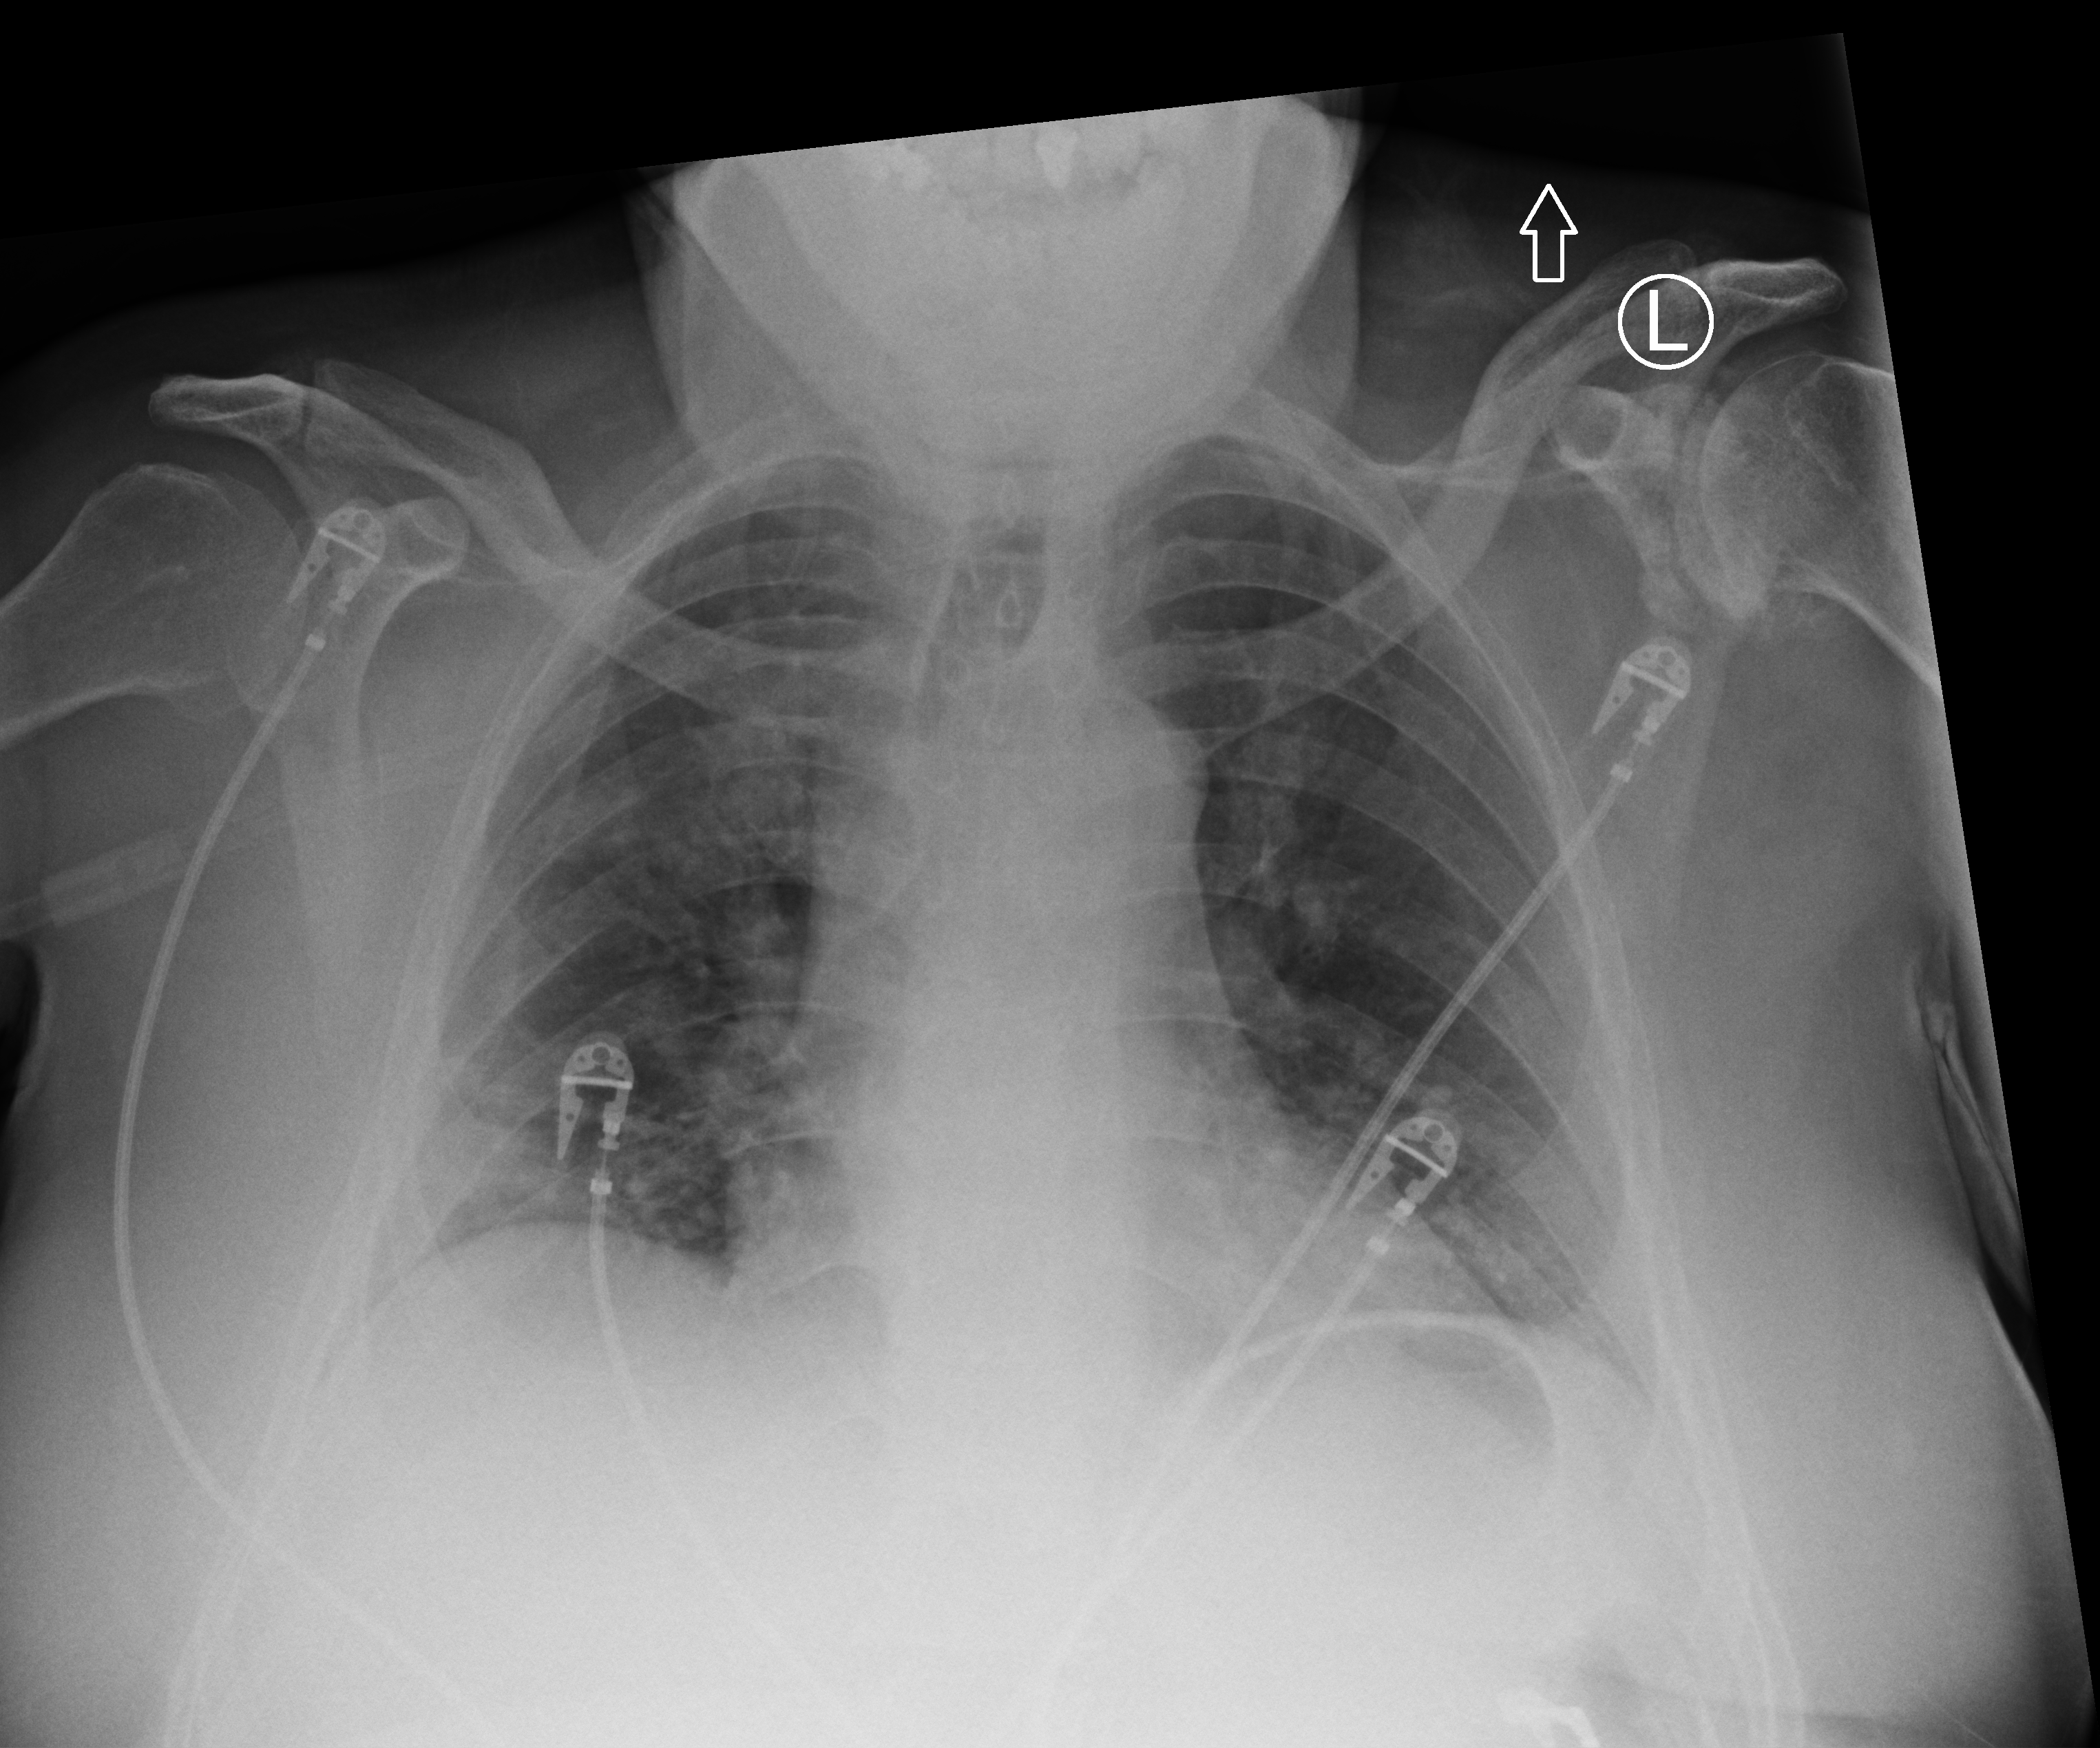
Chest X-ray (portable), anteroposterior (AP) projection. Male patient hospitalised with COVID-19, age 60–74 years.
Admission-level facts for this patient (not findings on this image; timing relative to this image not recorded):
- other chronic lung disease (admission record): no
- mechanically ventilated during this hospital stay: no